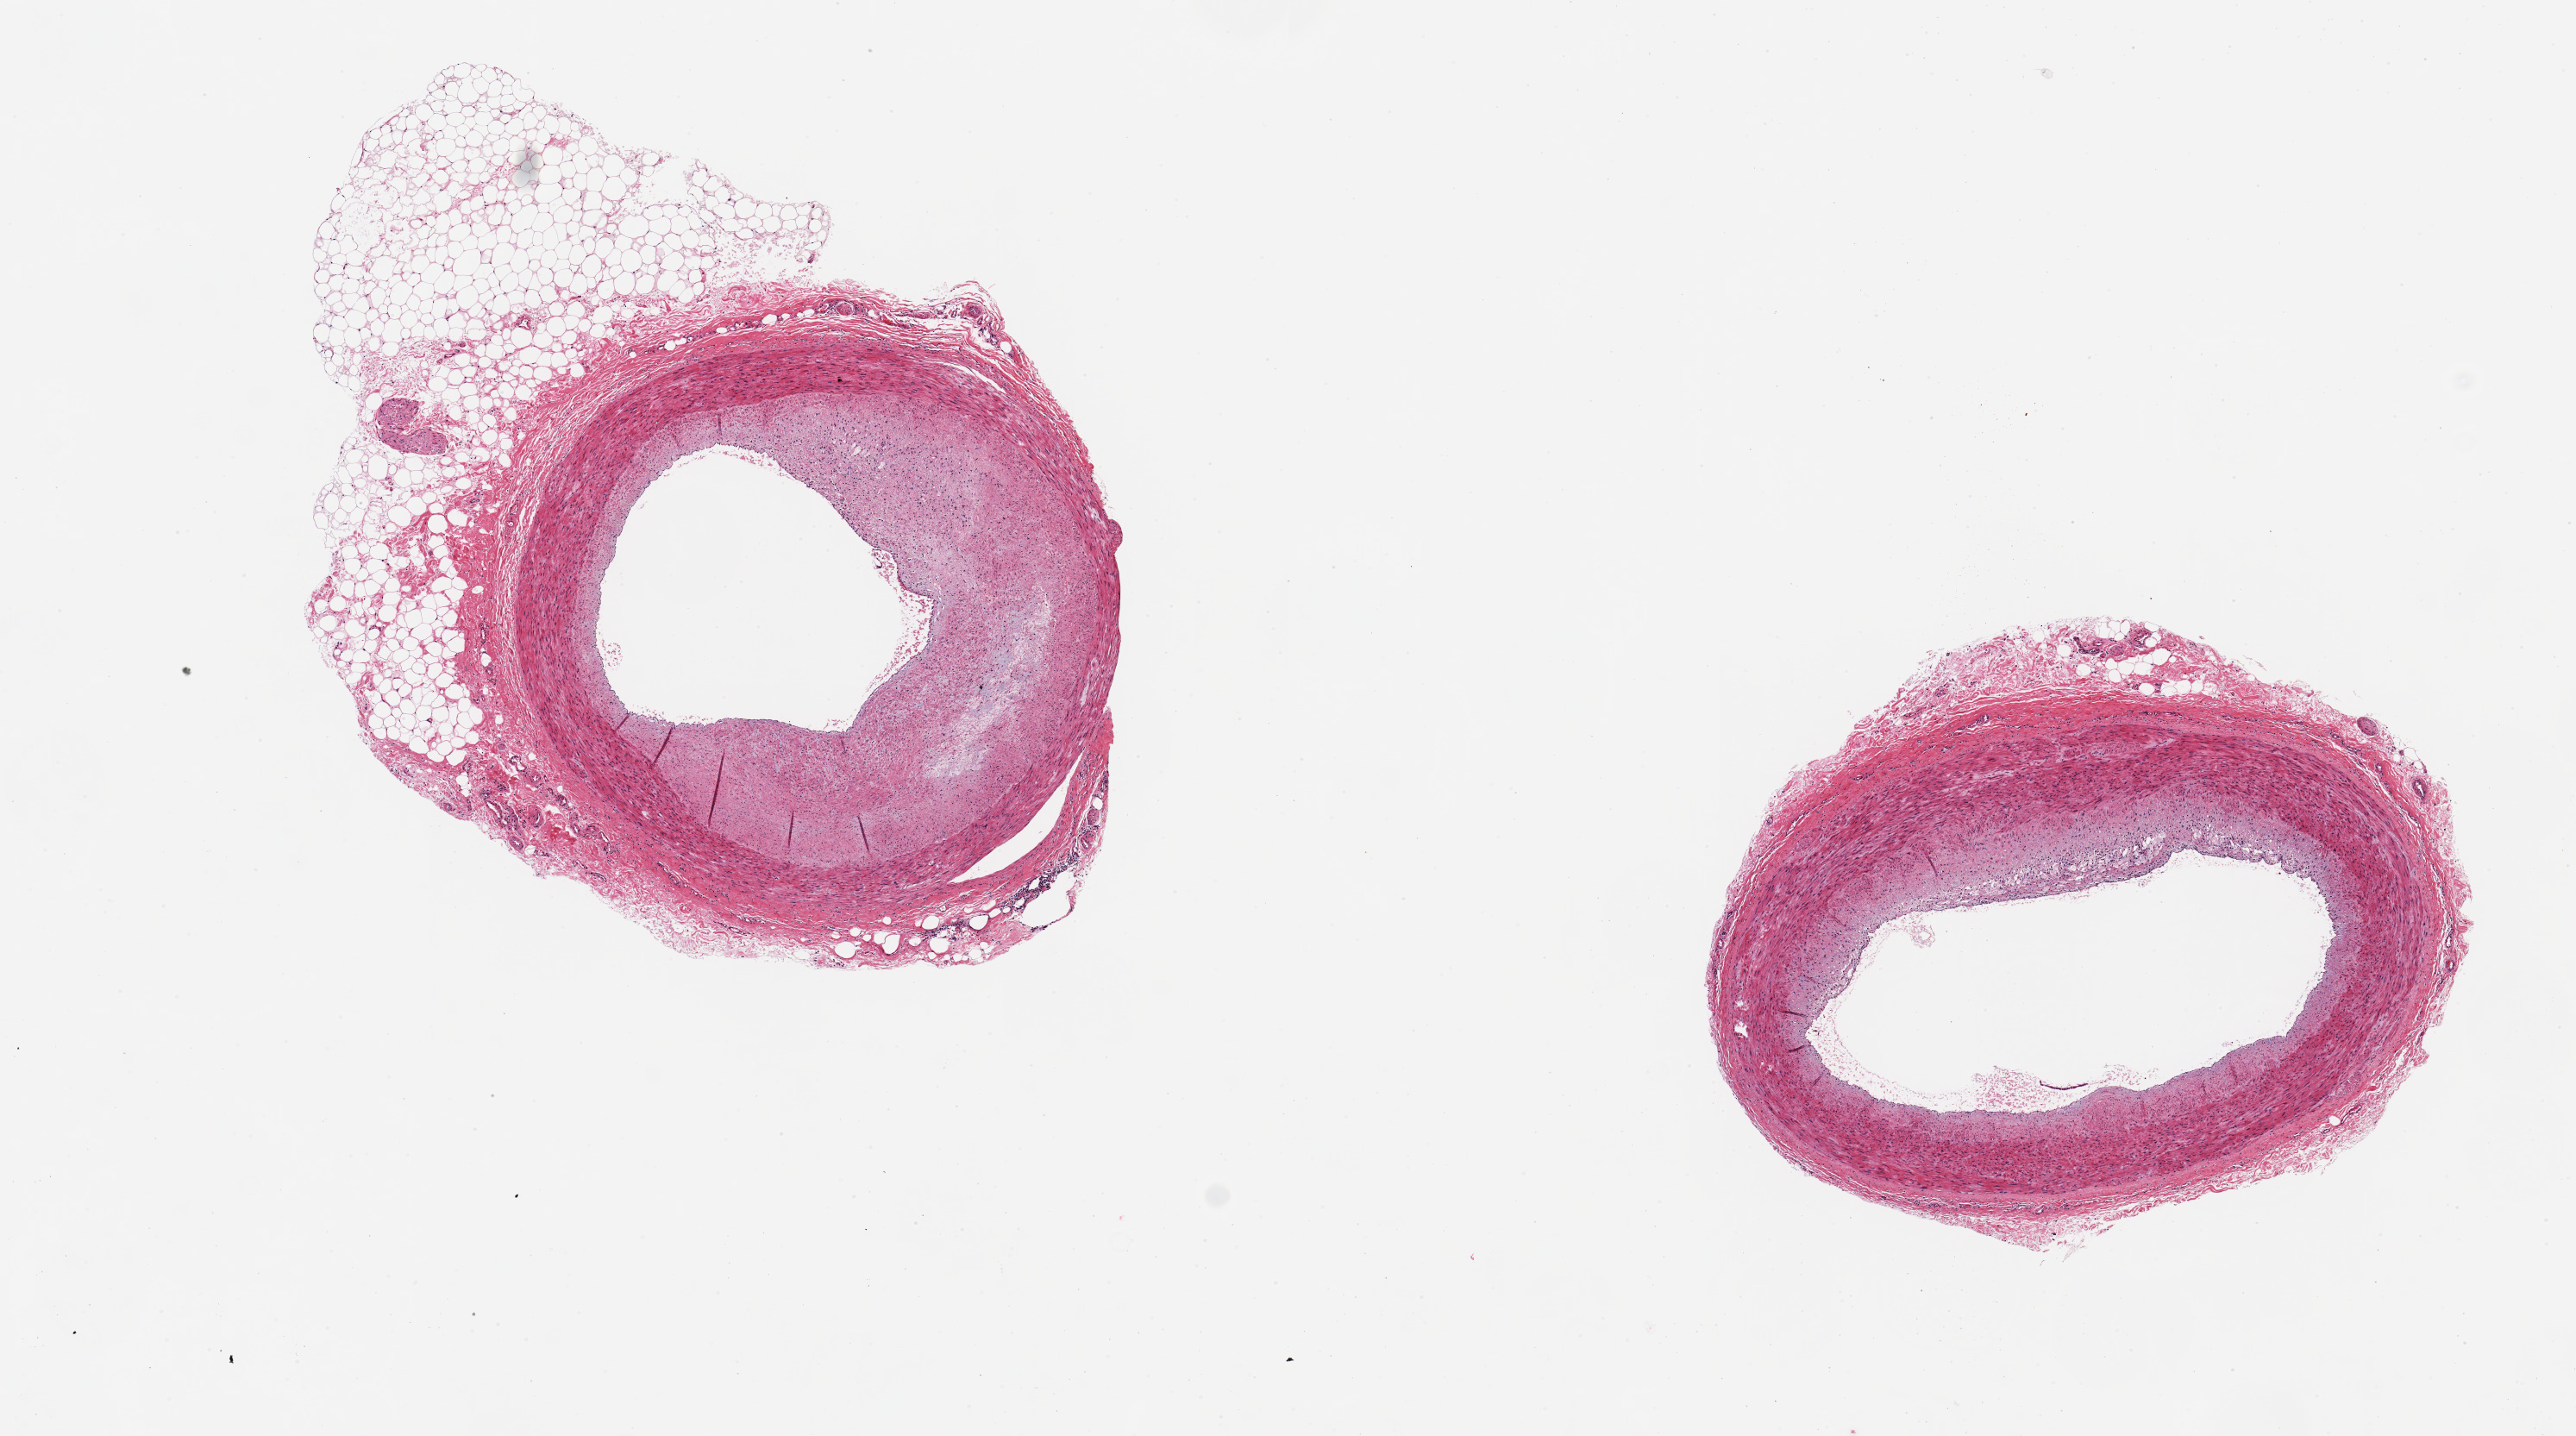
Digitized haematoxylin and eosin-stained section — shown as a low-resolution overview of the whole scanned area (about 11.8 x 6.6 mm); PAXgene-fixed paraffin-embedded (PFPE) section; target tissue: coronary artery; donor tissue sample. Donor: female.
- review note (as recorded): 2 pieces, 2.8mm diameter; 30% atherosclerotic plaque & 30% adipose in one; 20% plaque & <5% adipose in other